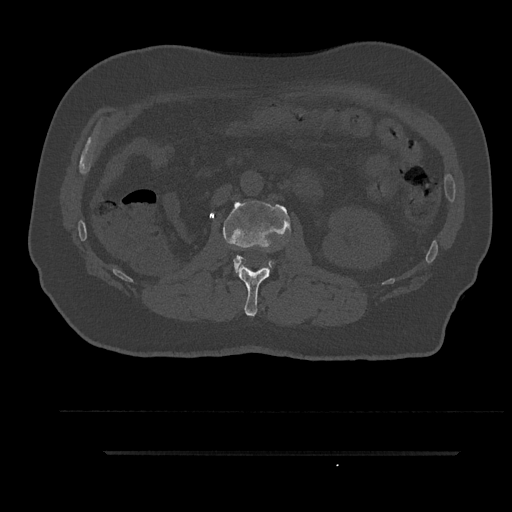
CT including the spine, one axial slice; slice 142 of 797 in the series (ordered by position); bone window (W 1800 / L 400 HU); 0.5 mm slice thickness; 512 × 512 image matrix. Male patient, age 63 years. Case-level facts recorded for this patient, not image findings: primary cancer: renal; vertebrae with lytic lesions (as recorded): T8.
Outlined on this slice (semi-automatic segmentation, software-assisted and operator-edited):
- L1 vertebra: box from (x=236, y=264) to (x=270, y=316) px
- L2 vertebra: (x=223, y=201)–(x=290, y=272)